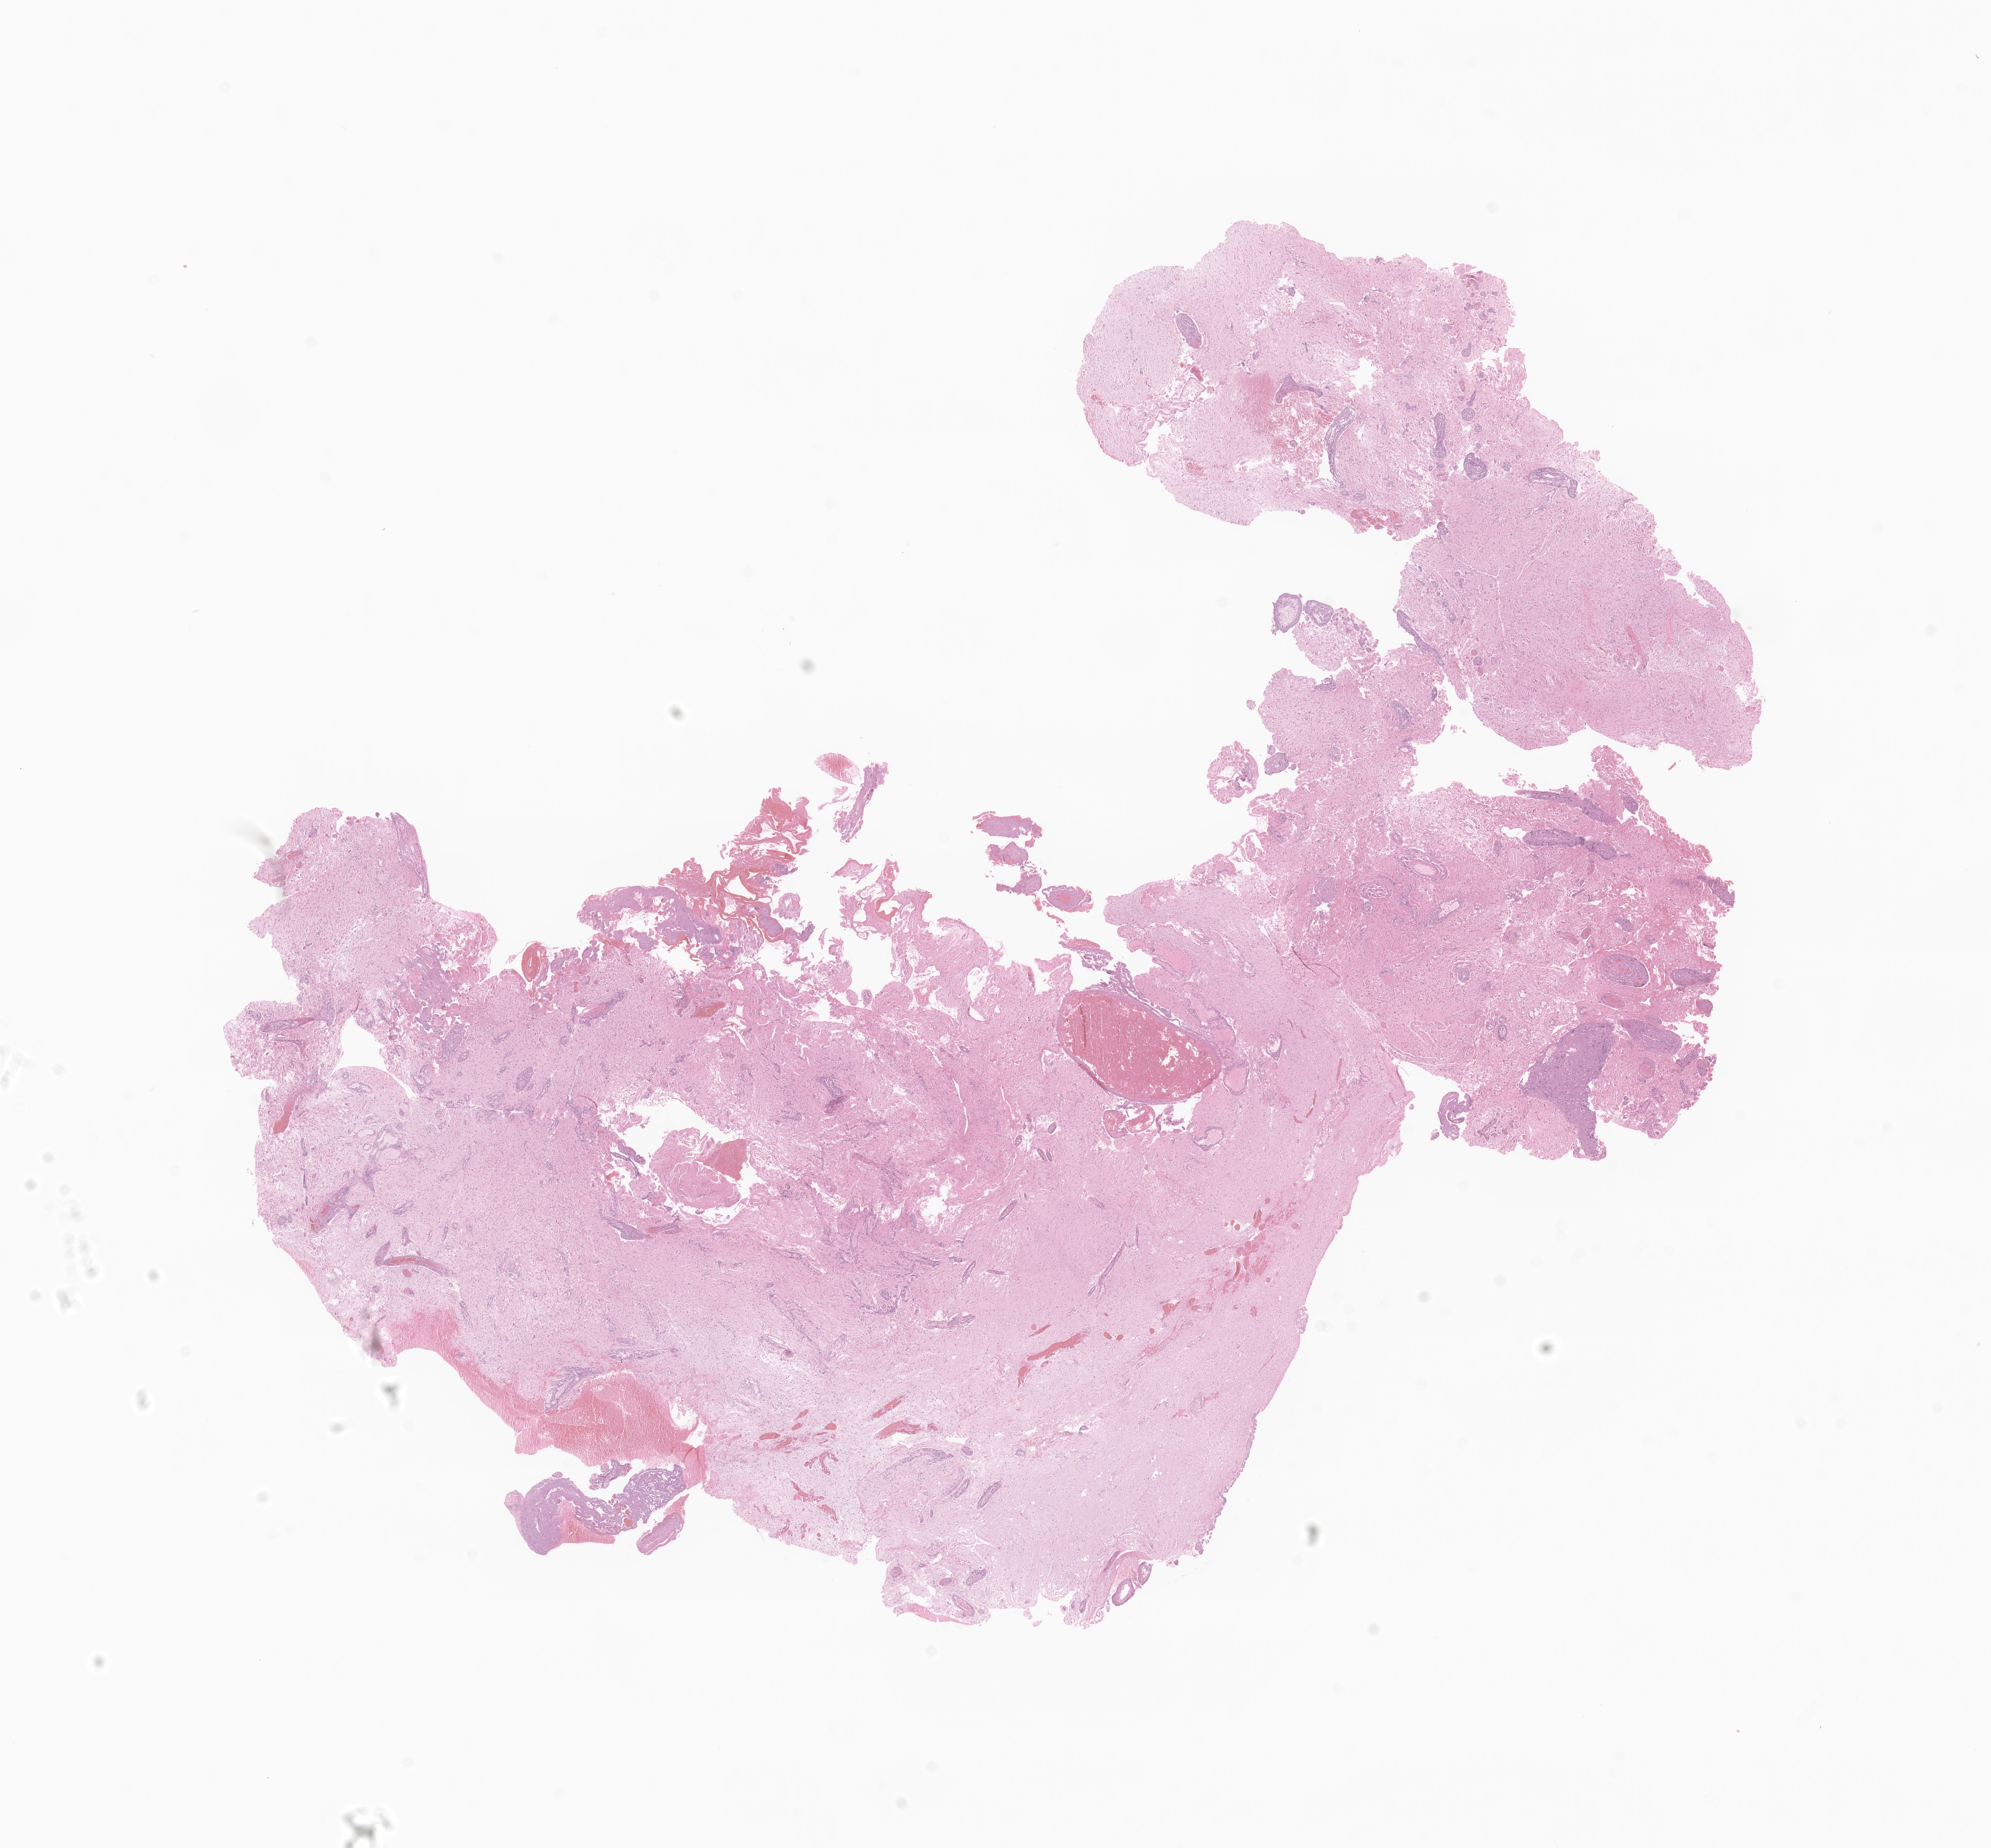
Digitized haematoxylin and eosin-stained section of tumor tissue from the brain, whole scanned area (about 16.4 x 15.3 mm) shown as a low-resolution overview, formalin-fixed paraffin-embedded section. Patient male; age 141 months (11 years 9 months).
Recorded diagnosis: Pilocytic astrocytoma.